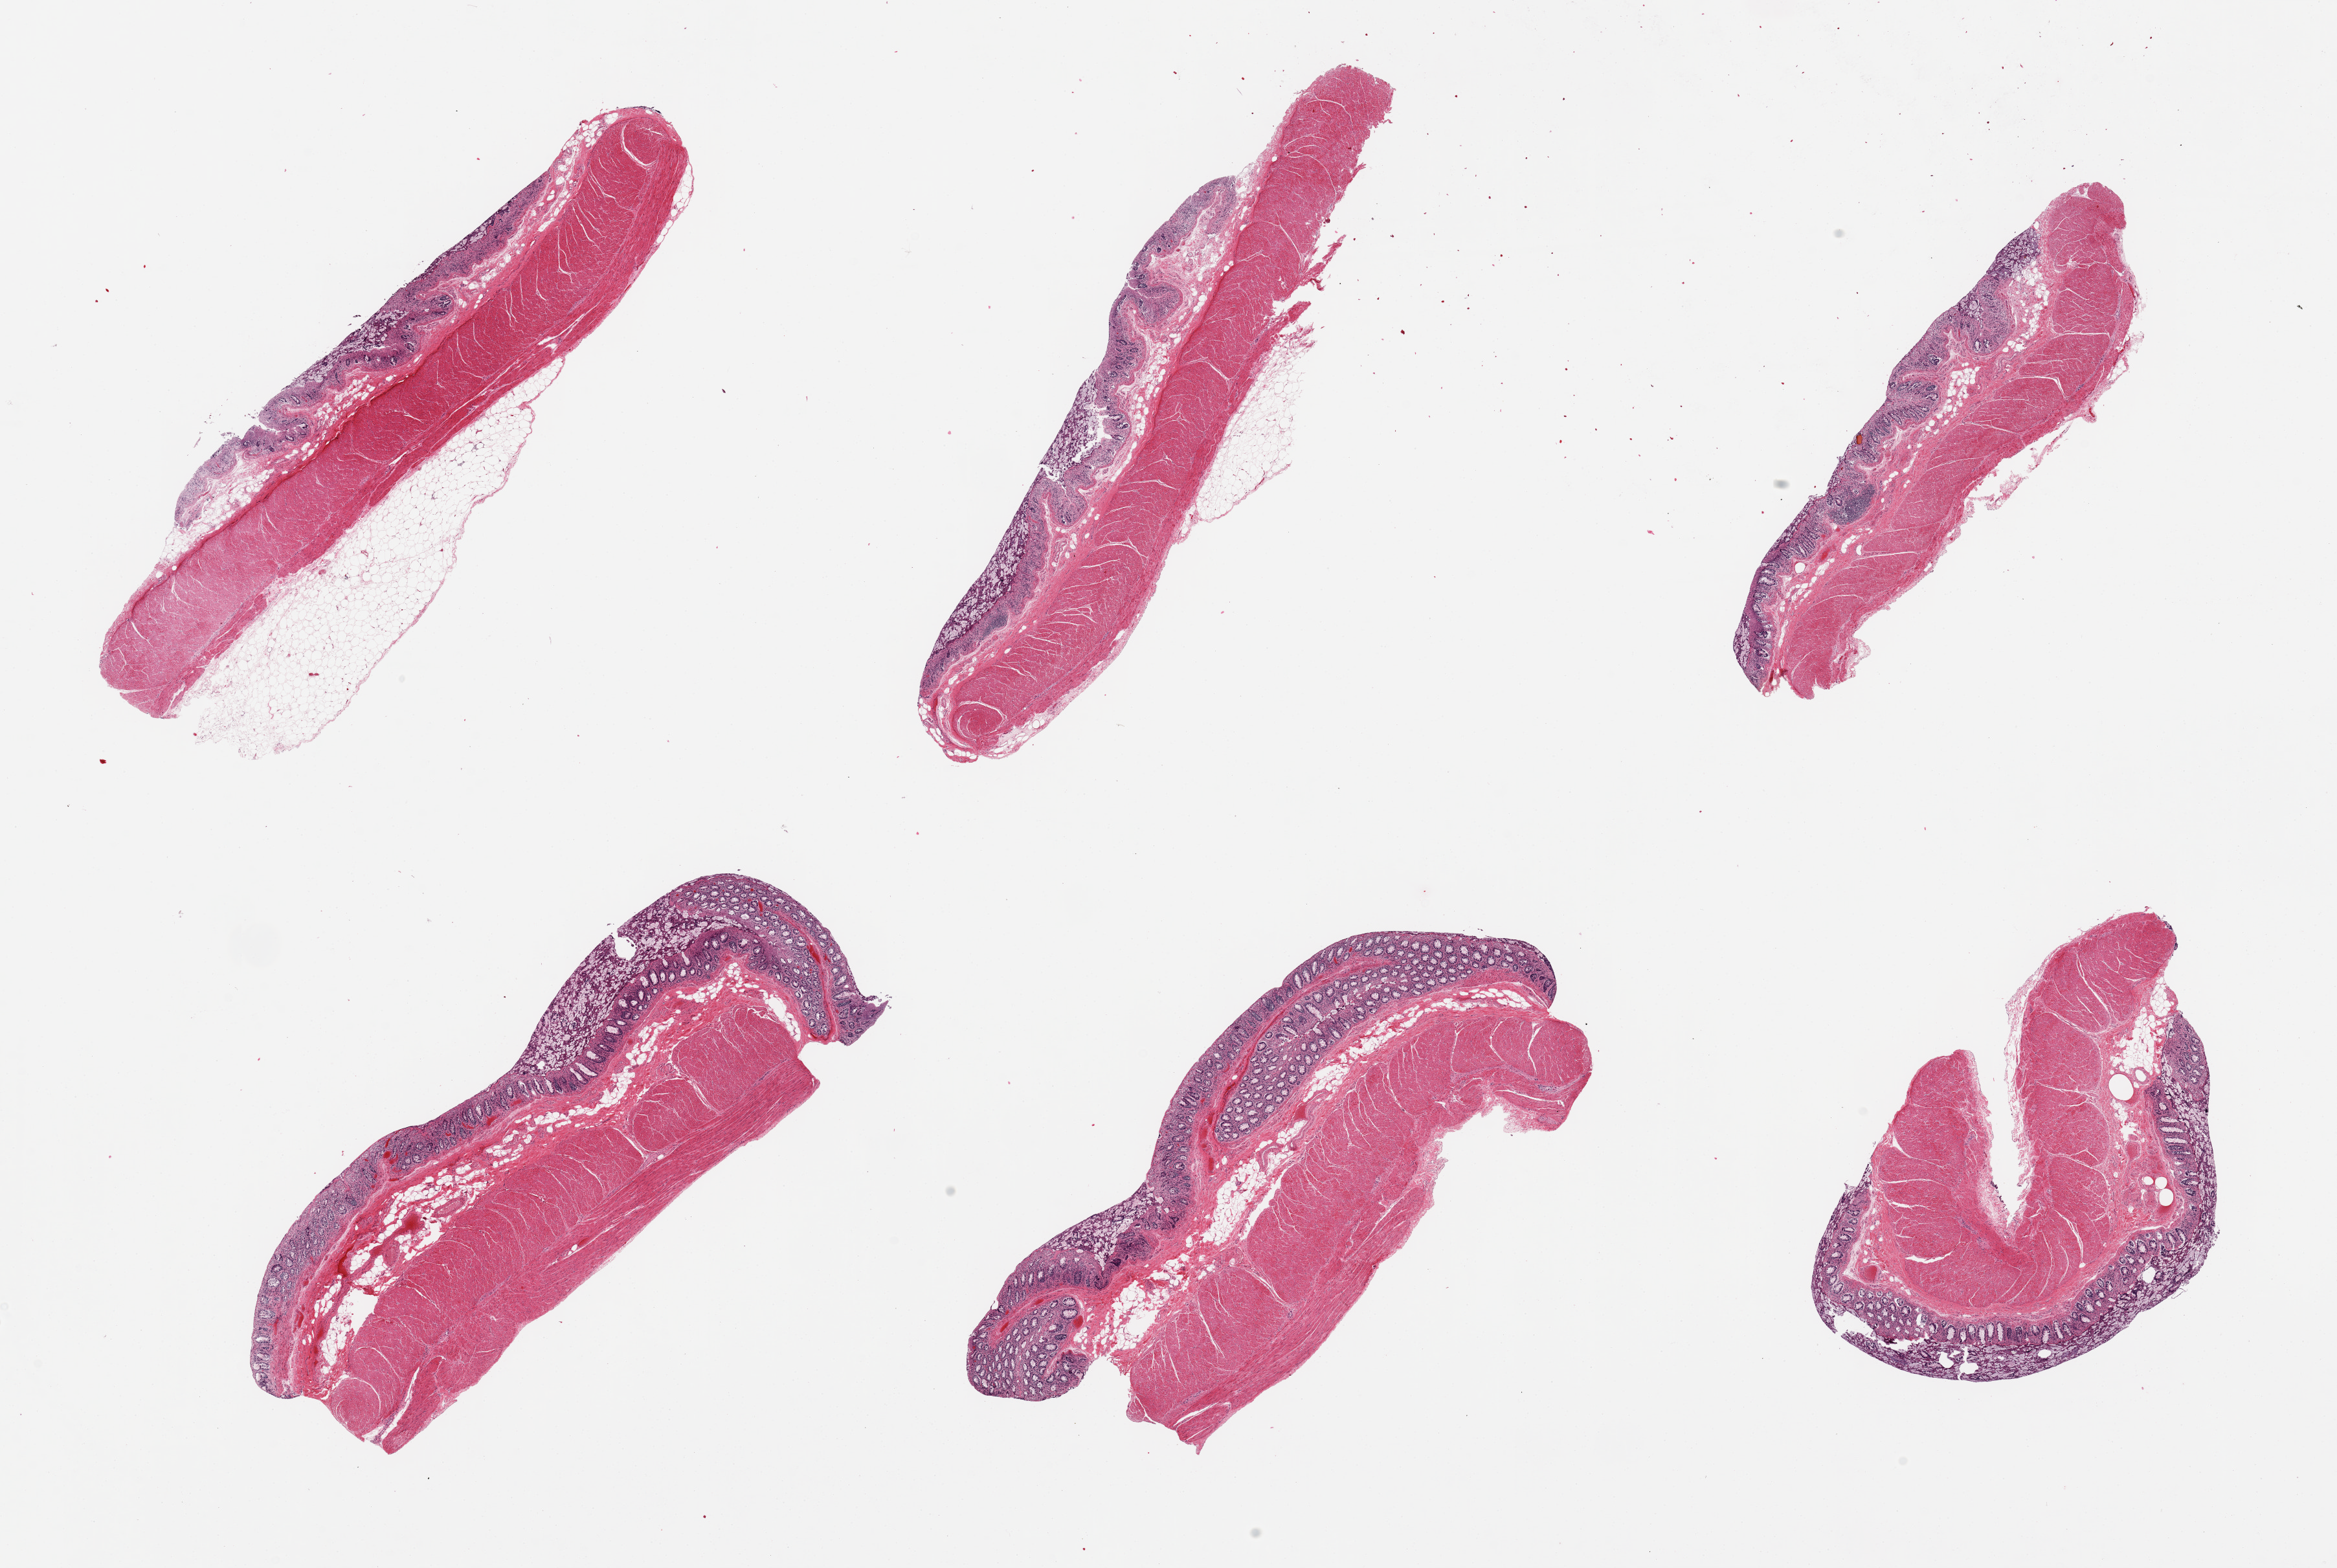
Digitized hematoxylin and eosin (H&E)-stained section — whole scanned area (about 28.5 x 19.2 mm, slide scanned at 20x) shown as a low-resolution overview, PAXgene-fixed paraffin-embedded (PFPE) section, sampled site (target tissue): transverse colon, donor tissue sample. Donor: male.
Review note (as recorded): 6pieces, mucosa is ~30% thickness, moderately-badly autolyzed.